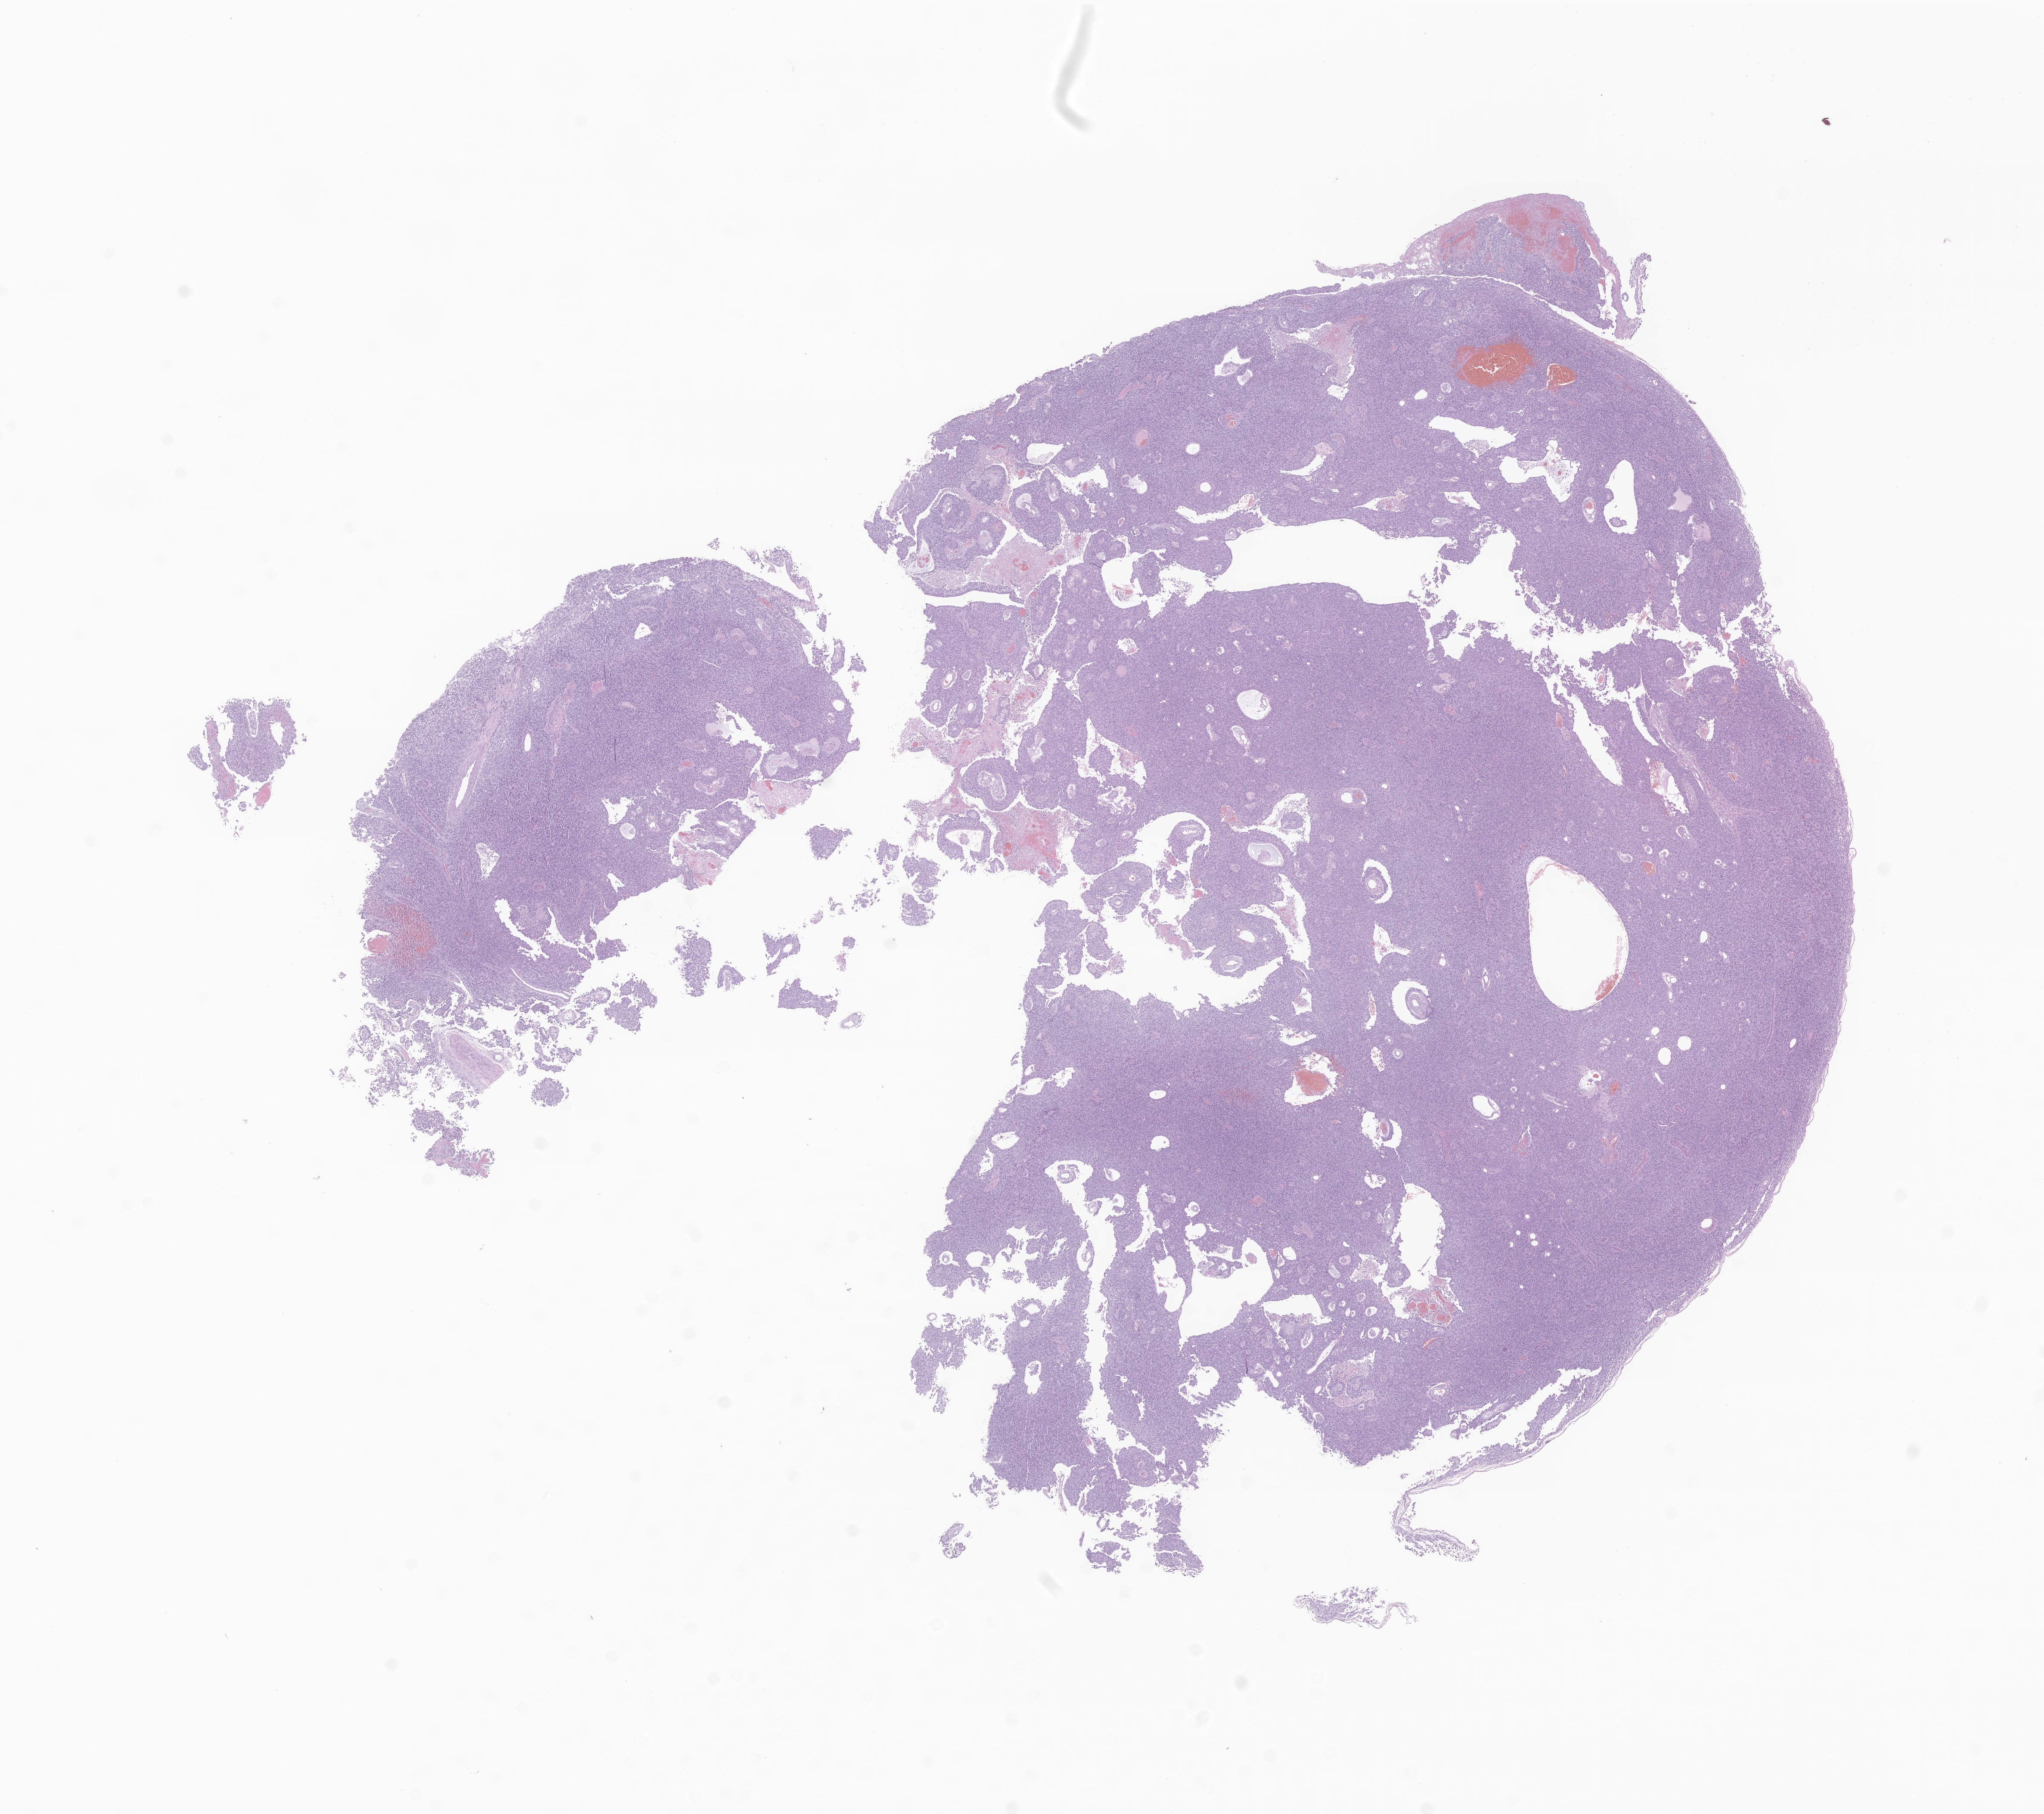
Whole-slide image, H&E stain of tumor tissue from the spinal cord, shown as a low-resolution overview of the whole scanned area (about 20.0 x 17.8 mm). Formalin-fixed, paraffin-embedded (FFPE) tissue. Patient male; age 128 months (10 years 8 months).
• diagnosis (ICD-O-3 morphology term): Ependymoma, NOS